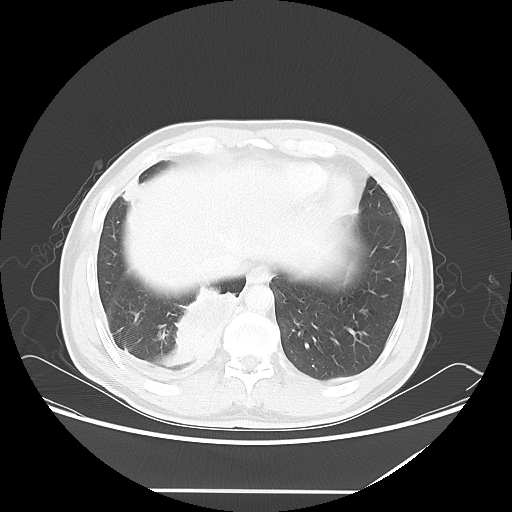
Chest CT, one axial slice. Position 16 of 60 along the scan axis. Reconstruction kernel LUNG. 120 kVp. Lung window (W 1500 / L -600 HU). 5 mm slice thickness. 512 × 512 image matrix, field of view 419 × 419 mm. Patient: male, 48 years. Case-level facts recorded for this patient, not image findings: clinical TNM (as recorded): T3 N3 M1a.
Outlined on this slice (rectangle marked by the reading radiologist):
- lung tumour (recorded histology: squamous cell carcinoma): bounding box [x1, y1, x2, y2] px = [162, 279, 234, 368]